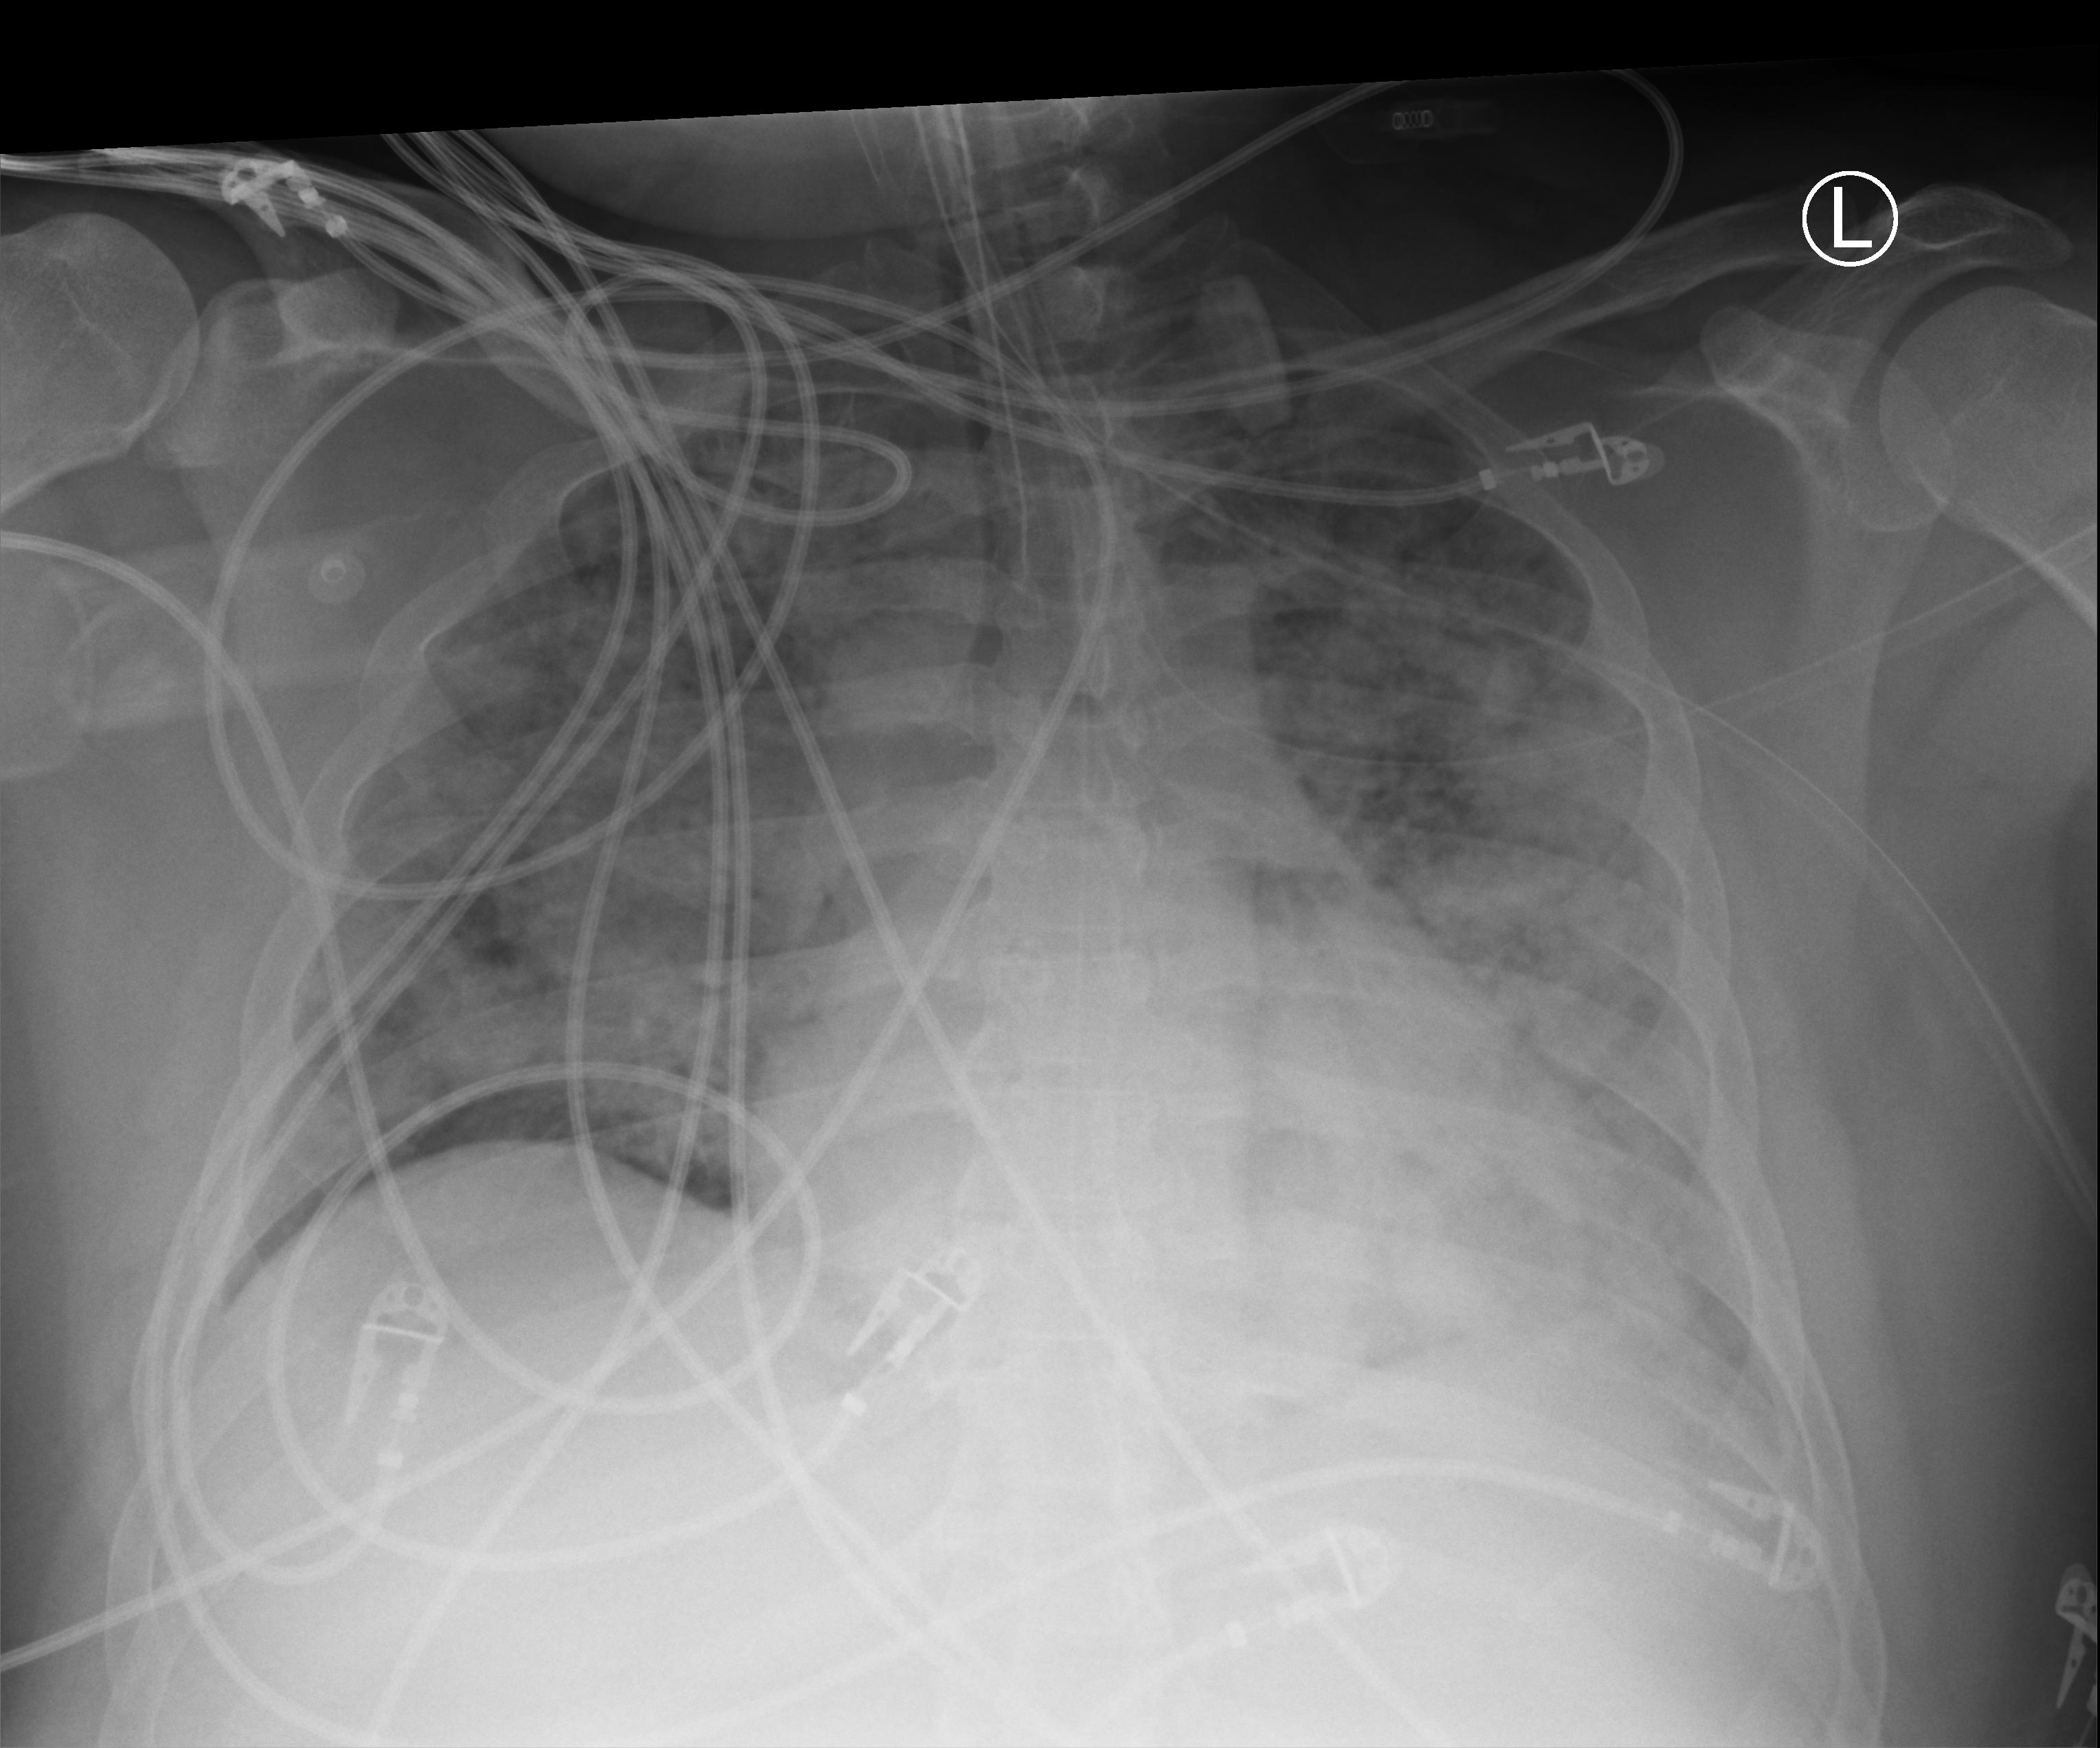
Portable chest radiograph; anteroposterior (AP) projection. Patient hospitalised with COVID-19, aged 18–59 years.
From the hospital-stay record, not from the radiograph (when in the stay this image was taken is not recorded): admitted to intensive care during this hospital stay: yes.